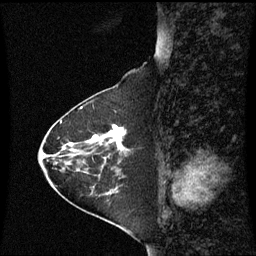
Breast MRI (dynamic contrast-enhanced), one sagittal slice. Slice 23 of 60 in the series (ordered by position). Dynamic contrast-enhanced series, image 2 of 3 at this slice position (ordered by acquisition). 1.5 T. TE 4.2 ms, TR 8.9 ms. 2 mm slice thickness. 256 × 256 image matrix. Female patient, age 63 years. From the clinical record (not read from this slice): setting: breast cancer imaged before/during neoadjuvant chemotherapy; receptor status: HR-positive, HER2-negative.
Structures marked on this image (semi-automatically segmented with operator editing):
- analysis volume of interest (the breast-tissue region the enhancement analysis was run in; not a lesion): box from (x=88, y=126) to (x=128, y=163) px
- tumour enhancement mask (voxels above the 70 % enhancement threshold inside the analysis volume of interest): (x=93, y=126)–(x=125, y=152)